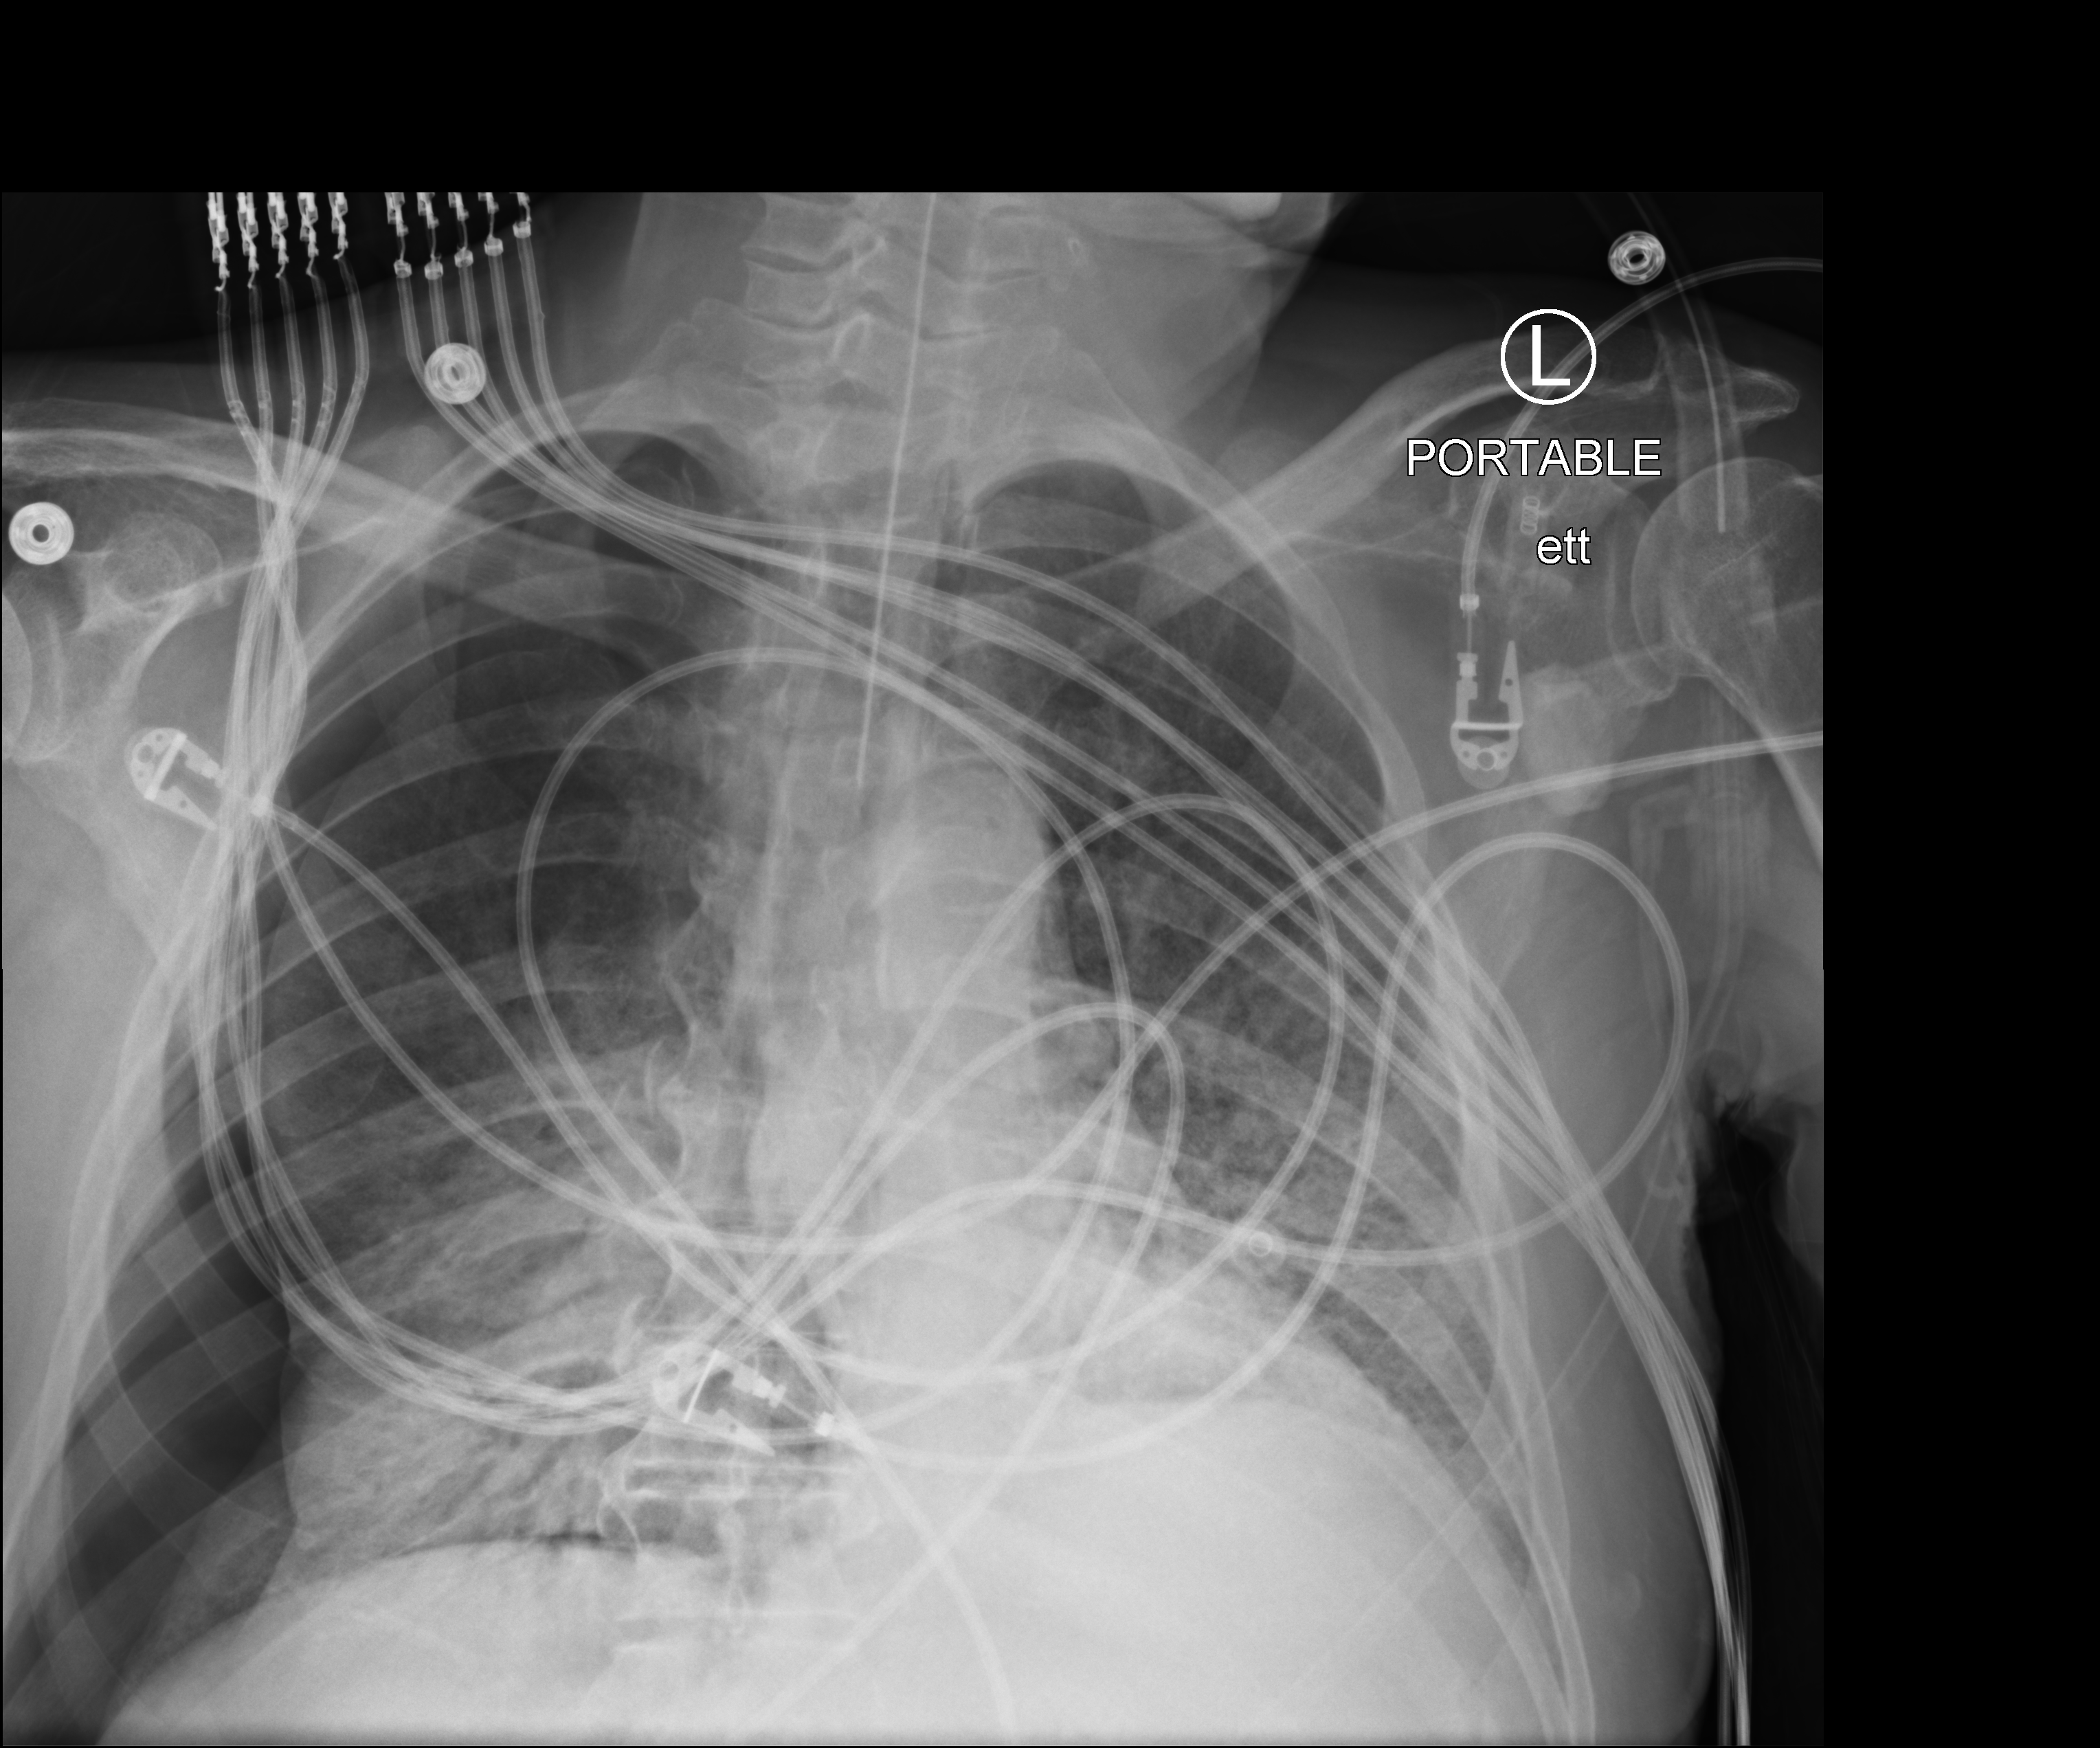
Chest X-ray (portable), anteroposterior (AP) projection. Patient hospitalised with COVID-19; male, aged 75–90 years.
Admission-level facts for this patient (not findings on this image; timing relative to this image not recorded):
- admitted to intensive care during this hospital stay: yes
- other chronic lung disease (admission record): no
- length of hospital stay: 23 days